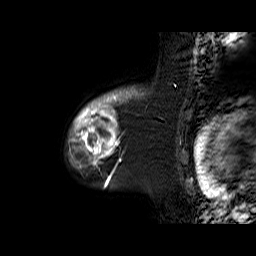
Breast MRI (dynamic contrast-enhanced), one sagittal slice. Slice 52 of 60 in the series (ordered by position). Dynamic contrast-enhanced series, time point 2 of 6 at this slice position (early post-contrast). 1.5 T. TE 6.3 ms, TR 32.9 ms. 4 mm slice thickness. 256 × 256 image matrix, field of view 200 × 200 mm. Female patient. Case-level facts recorded for this patient, not image findings: setting: breast cancer imaged before/during neoadjuvant chemotherapy; receptor status: triple-negative.
Annotated regions visible in this slice (semi-automatic segmentation, software-assisted and operator-edited):
- analysis volume of interest (the breast-tissue region the enhancement analysis was run in; not a lesion): bounding box <68,91,141,170> (left, top, right, bottom; pixels)
- tumour enhancement mask (voxels above the 100 % enhancement threshold inside the analysis volume of interest): <69,91,126,170>